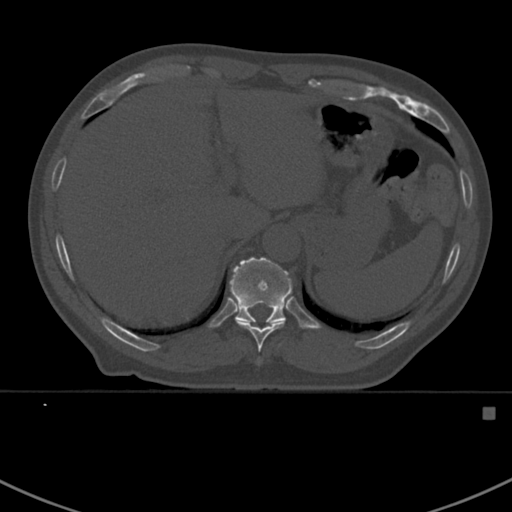
CT including the spine, one axial slice. Slice 358 of 412 in the series (ordered by position). Reconstruction kernel Br40s. Bone window (W 1800 / L 400 HU). 512 × 512 image matrix, field of view 358 × 358 mm. Patient: male, 59 years. From the clinical record (not read from this slice): primary cancer: prostate.
Outlined on this slice (semi-automatic segmentation, software-assisted and operator-edited):
- T10 vertebra: bounding box <235,321,285,363> (left, top, right, bottom; pixels)
- T11 vertebra: <230,257,302,328>